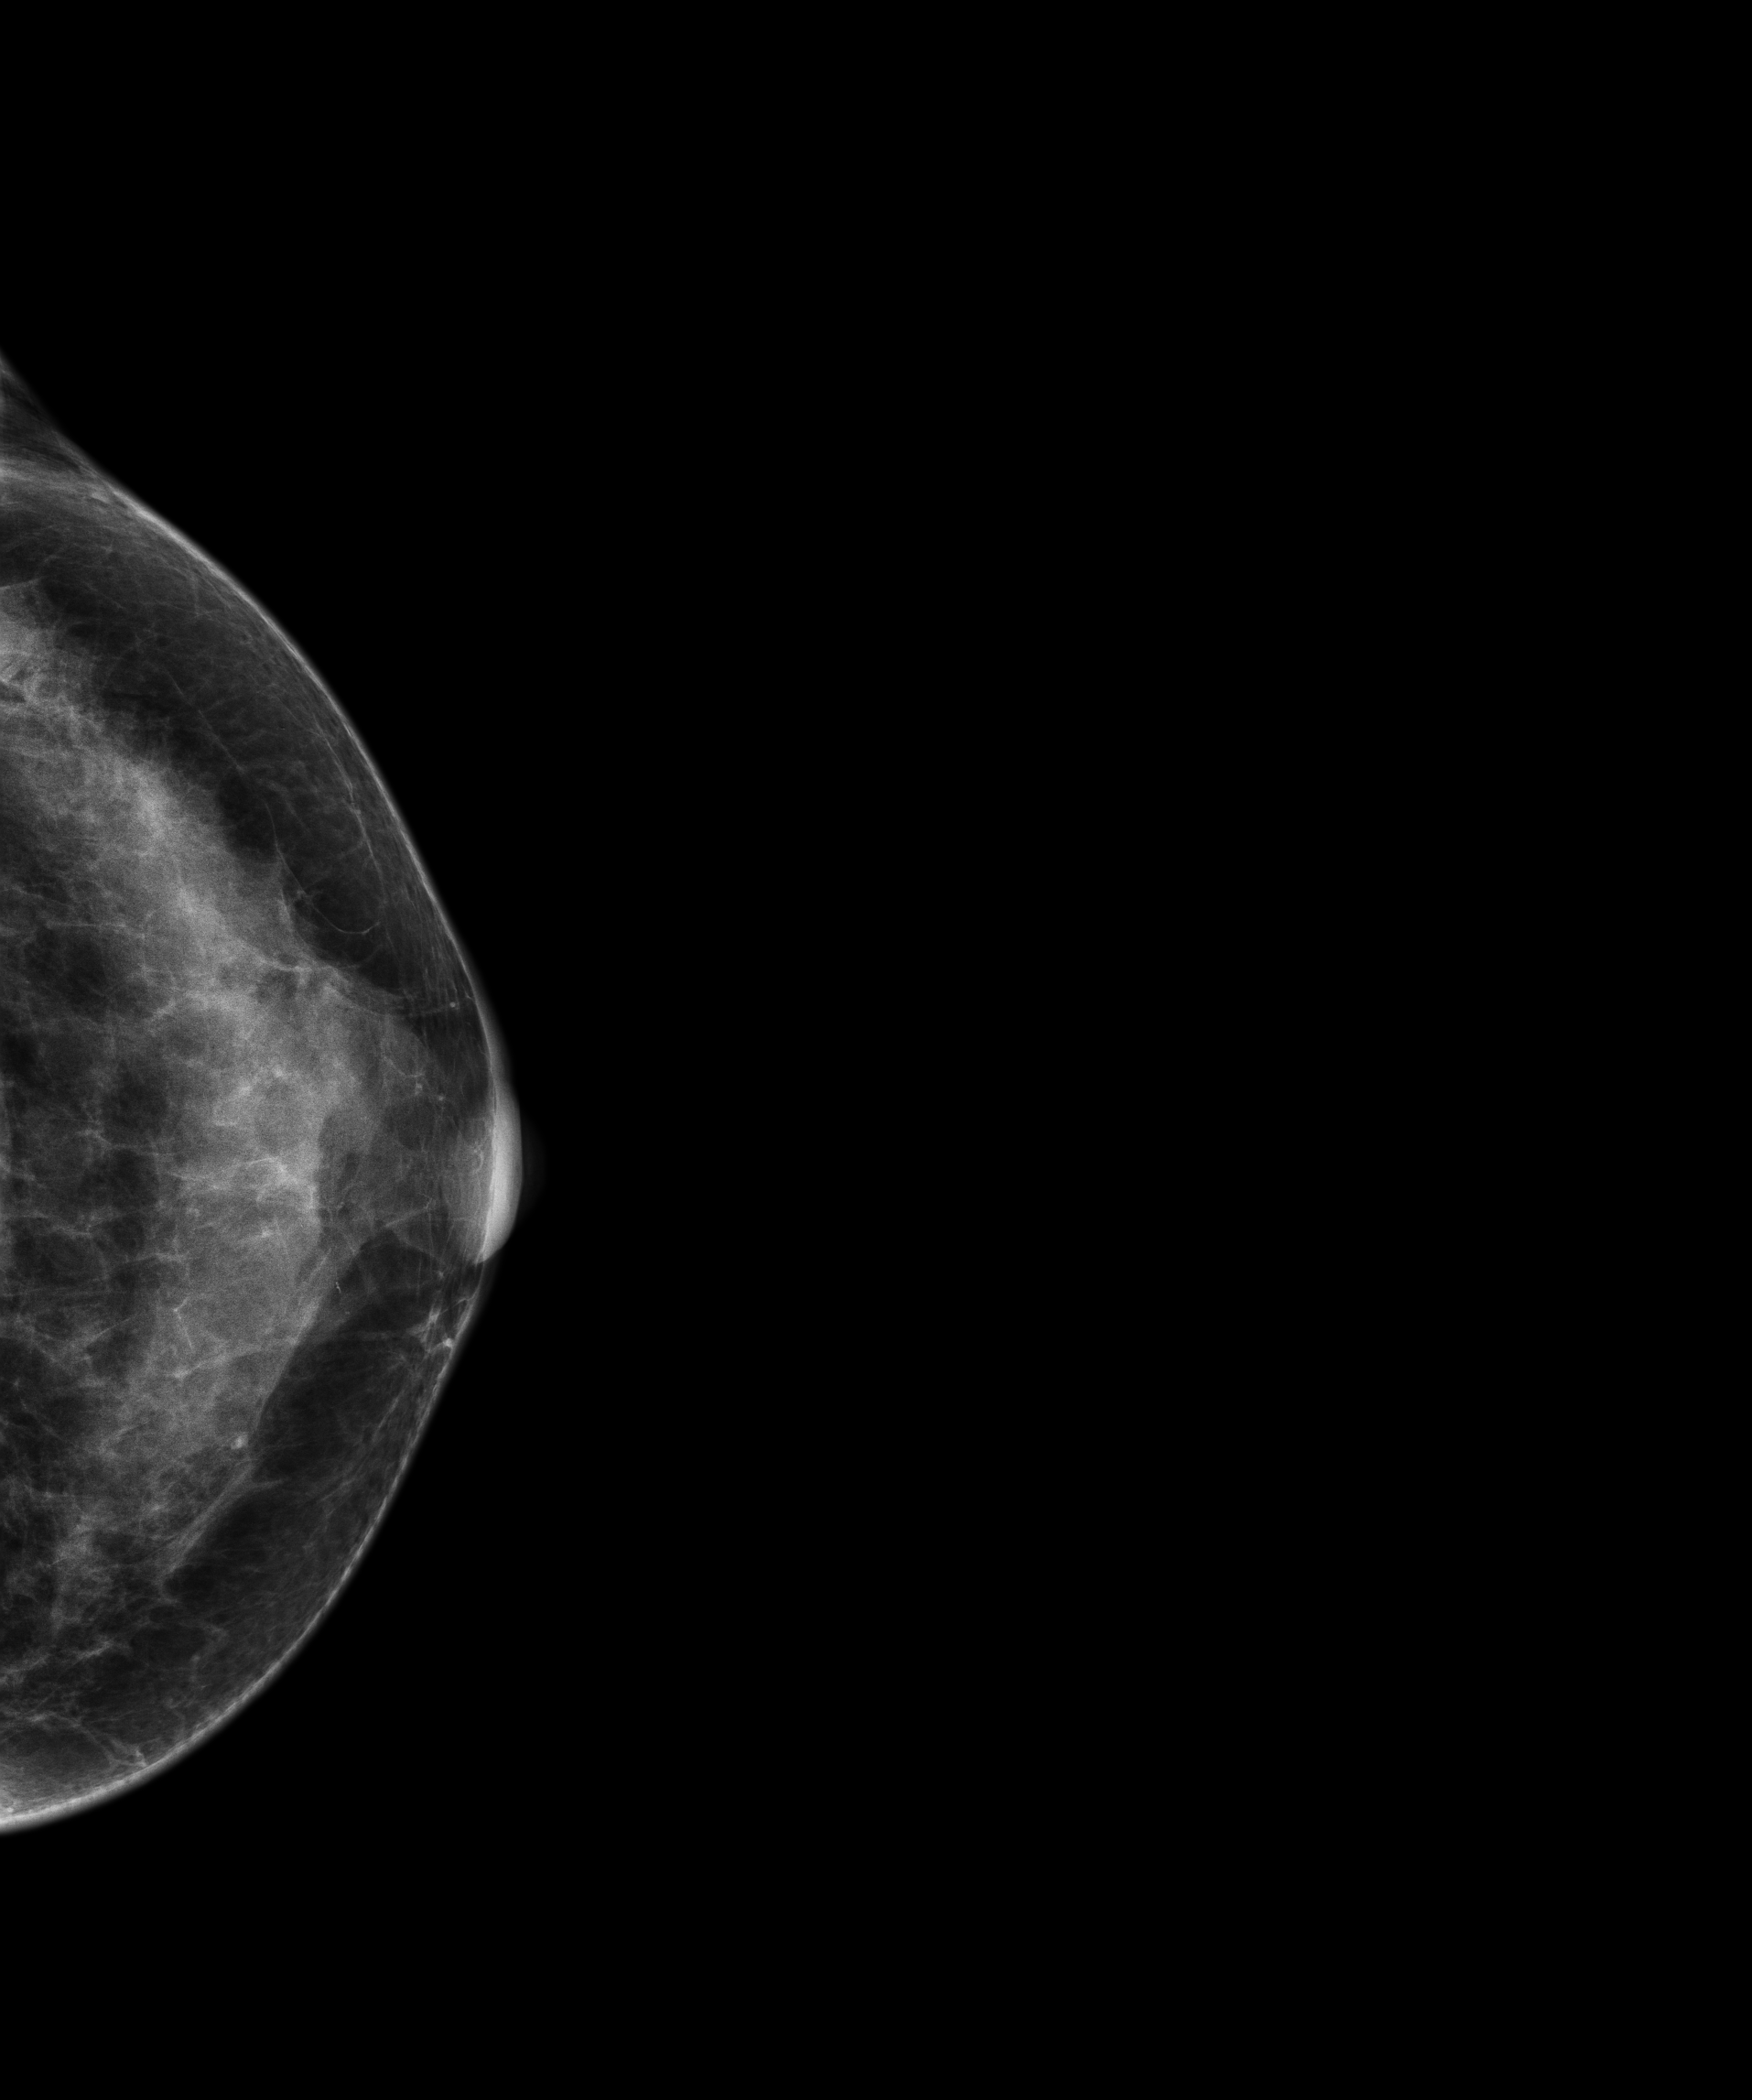
Full-field digital mammogram (FFDM); left breast; CC view; annual screening mammography examination. Female patient, age 46 years.
BI-RADS breast density category at the screening exam (both breasts, scale 1–4): 4. Final BI-RADS assessment for this screening round (tomosynthesis exam, both breasts): category 1. Recall: no recall after this screen.